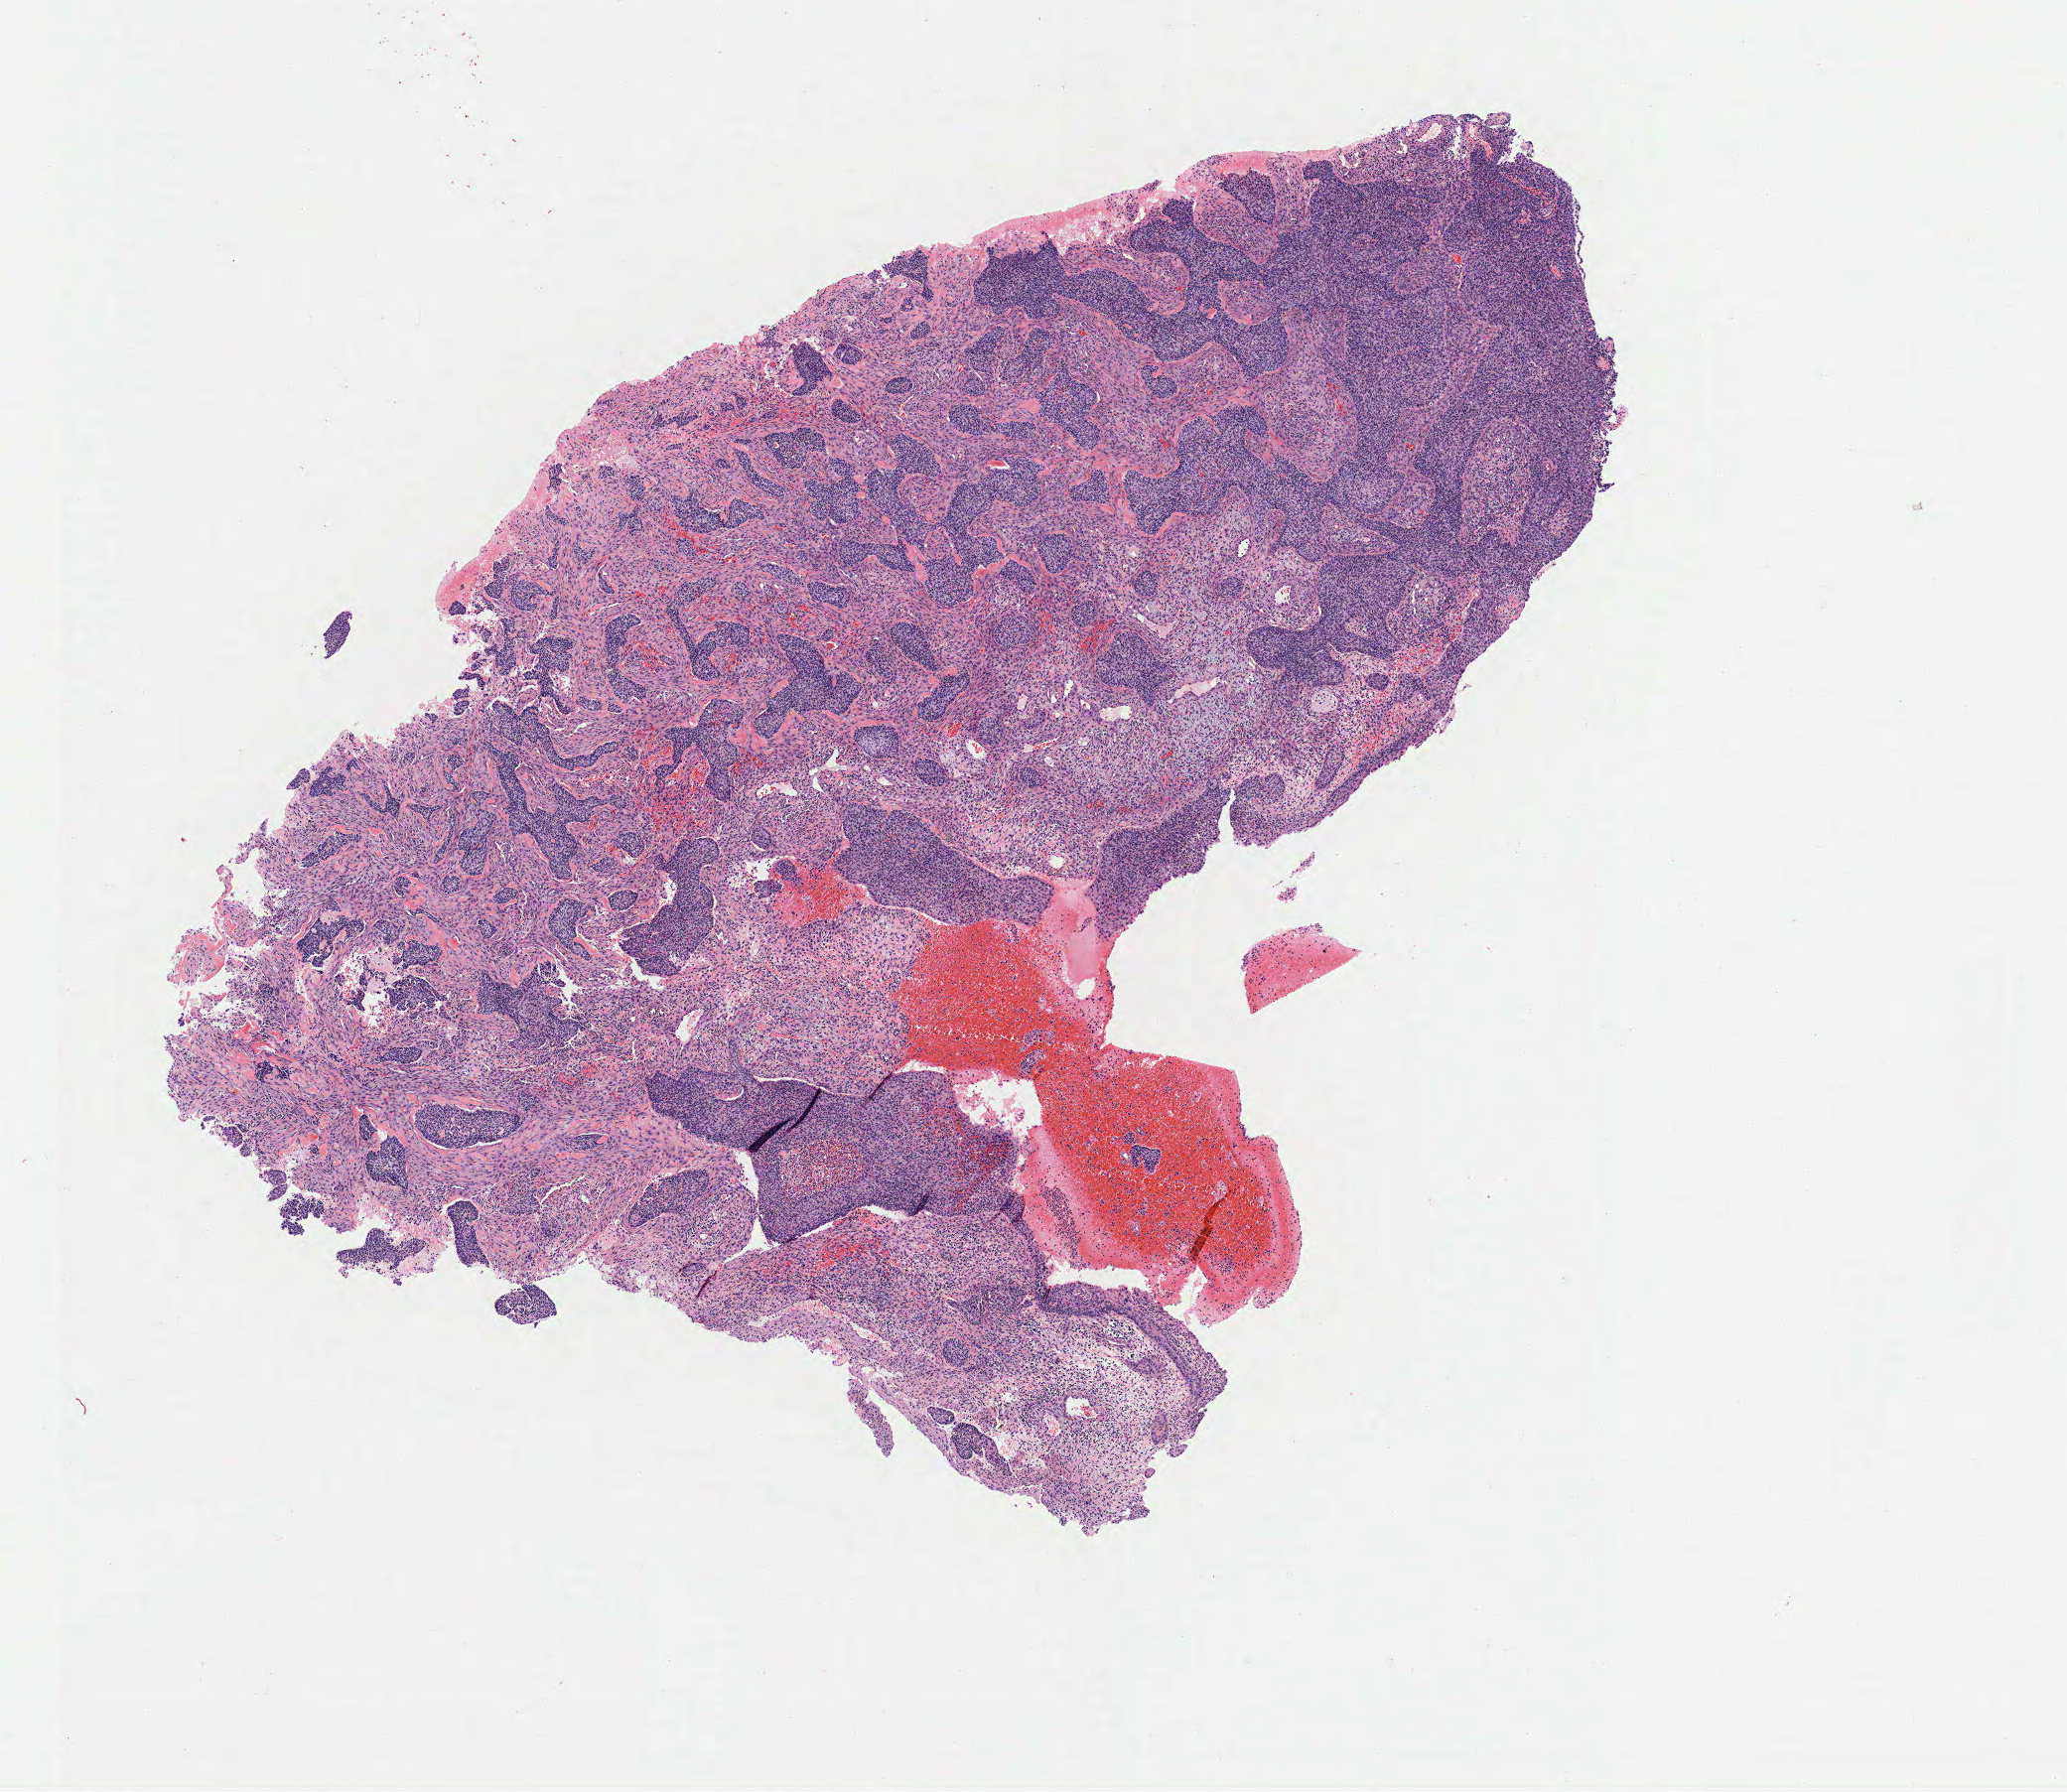
Whole-slide image, hematoxylin and eosin (H&E) stain, low-resolution overview of the scanned area, about 8.2 x 7.1 mm. Tumor tissue. Site: cervix. Patient: female, aged 44.
* histologic diagnosis: Squamous cell carcinoma, large cell, nonkeratinizing, NOS